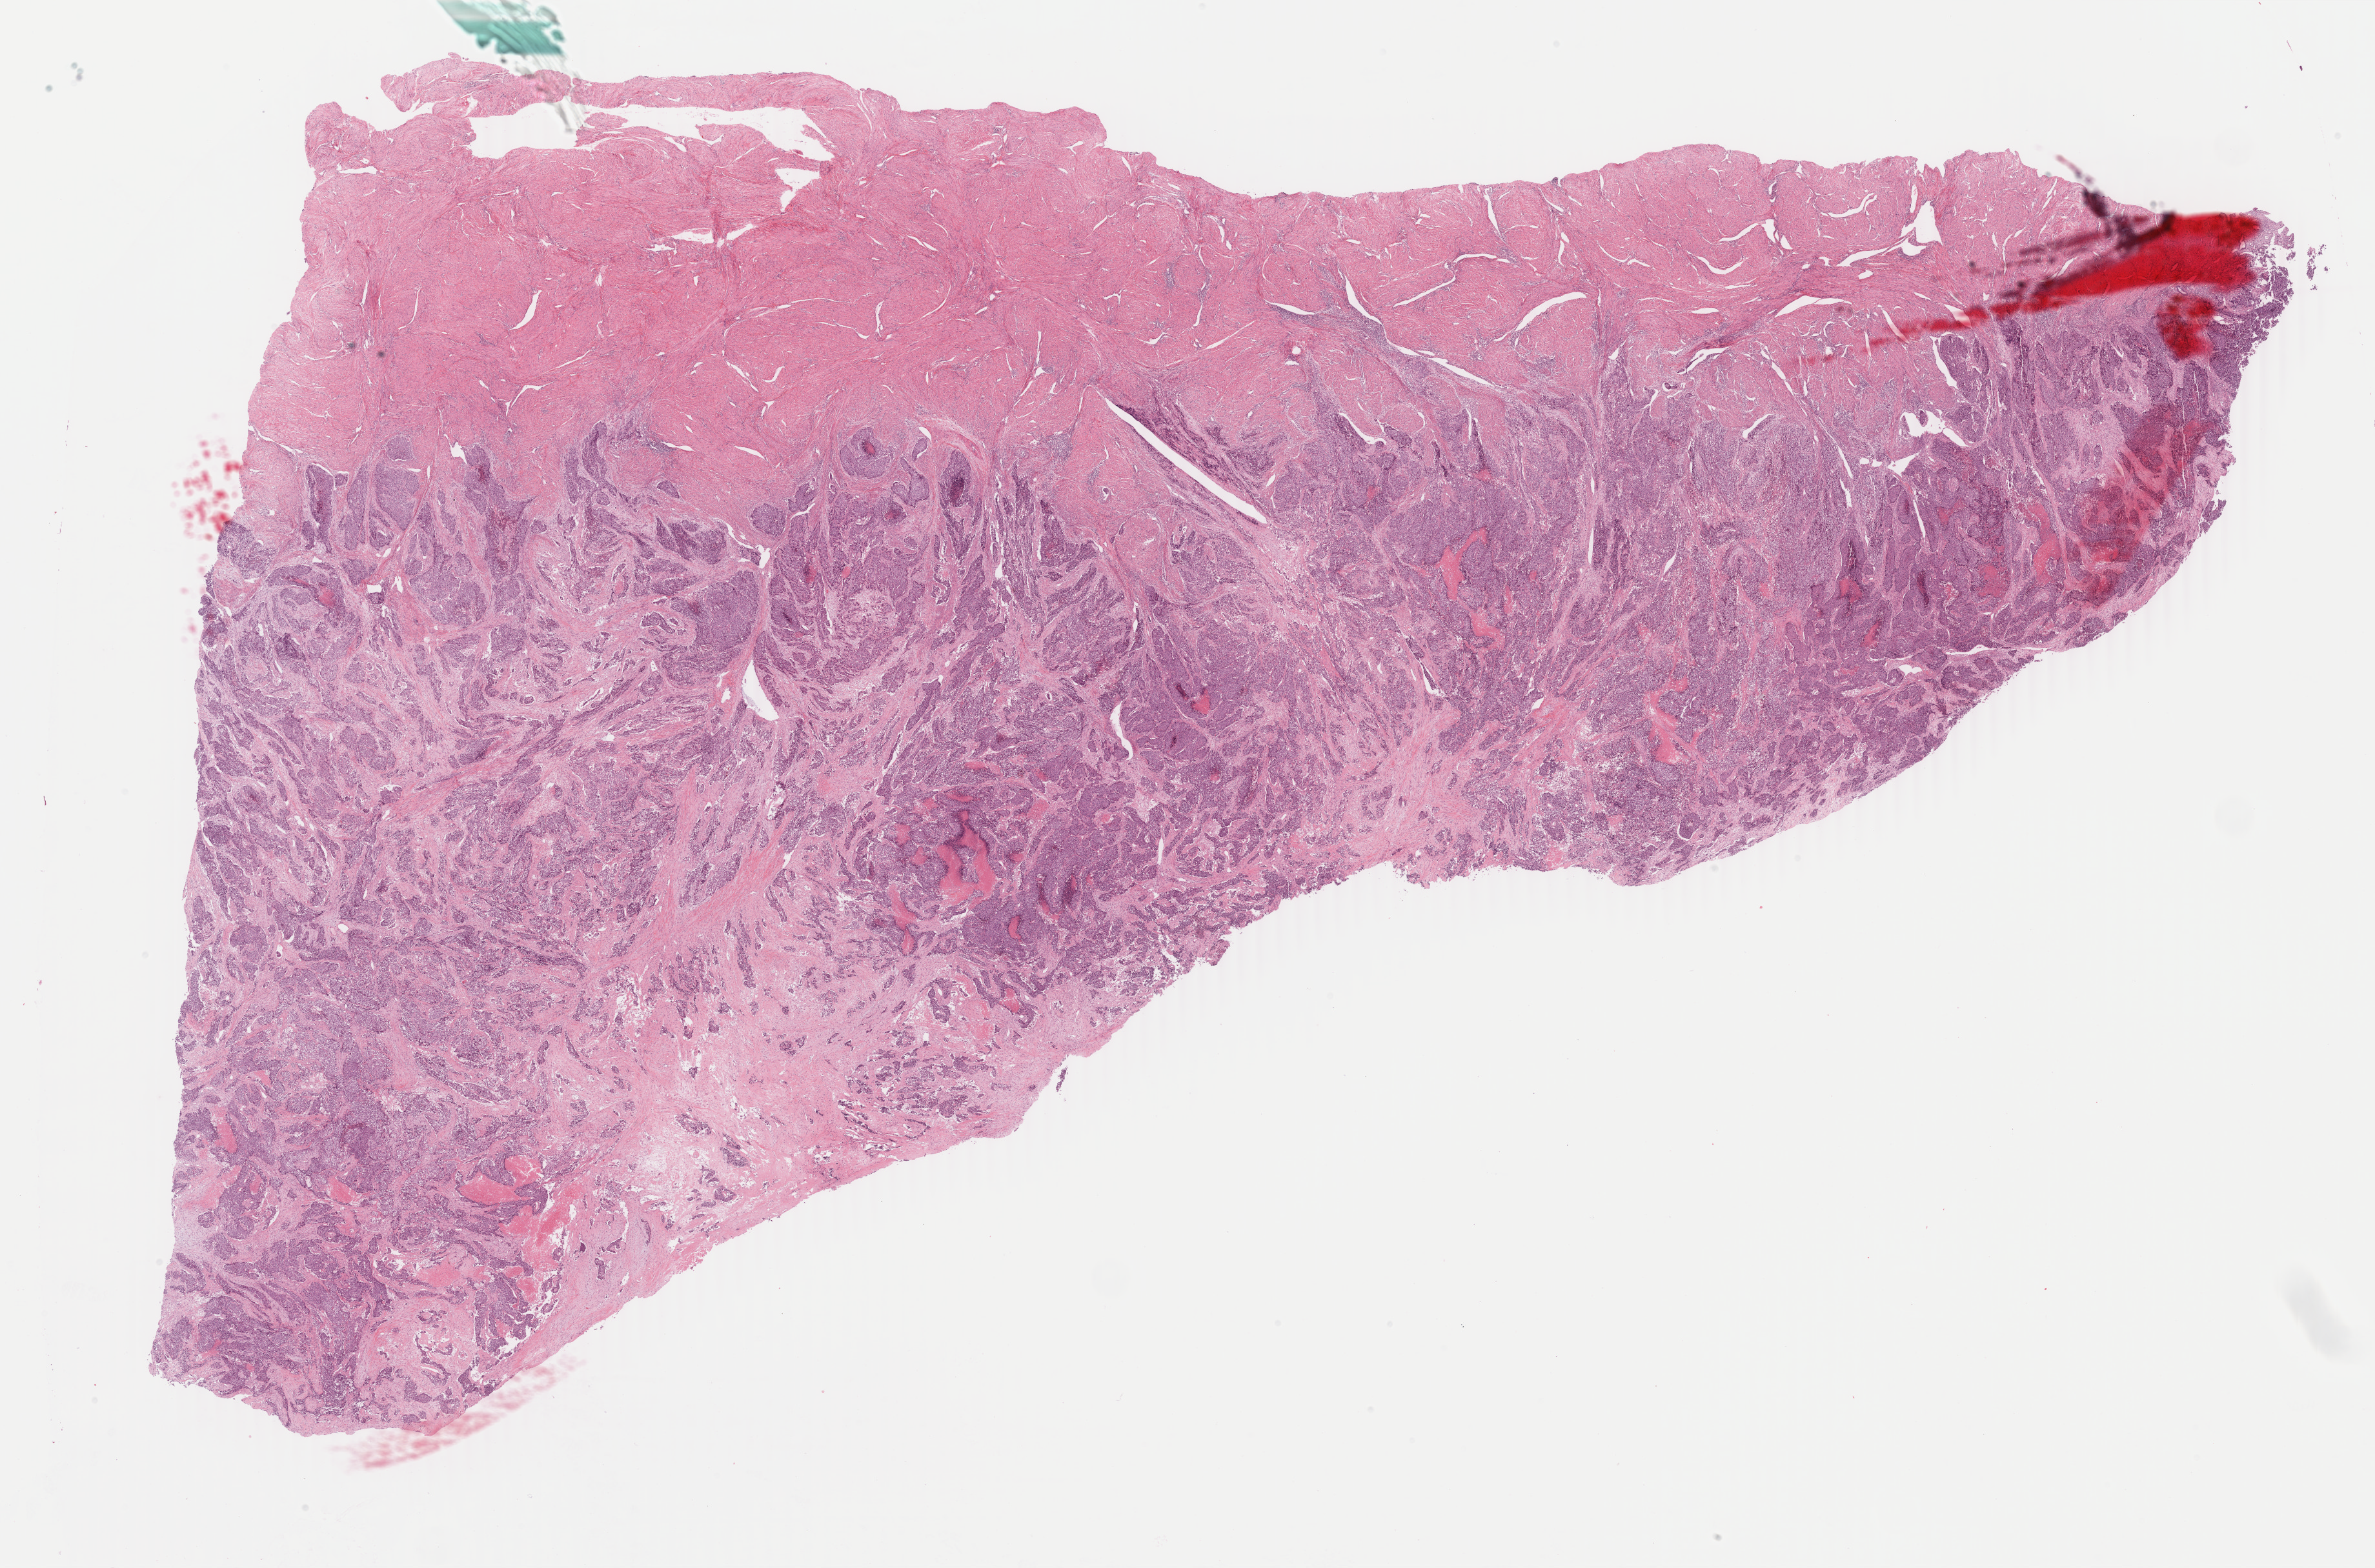
H&E whole-slide image, whole scanned area (about 29.3 x 19.3 mm, acquisition: 40x scan) shown as a low-resolution overview. FFPE section. Sample: primary tumour, cervix. Female, age 51 years at initial diagnosis. Histologic grade: G2 (moderately differentiated).
- FIGO stage: IIA2
- diagnosis: Squamous cell carcinoma, NOS (cervix uteri)